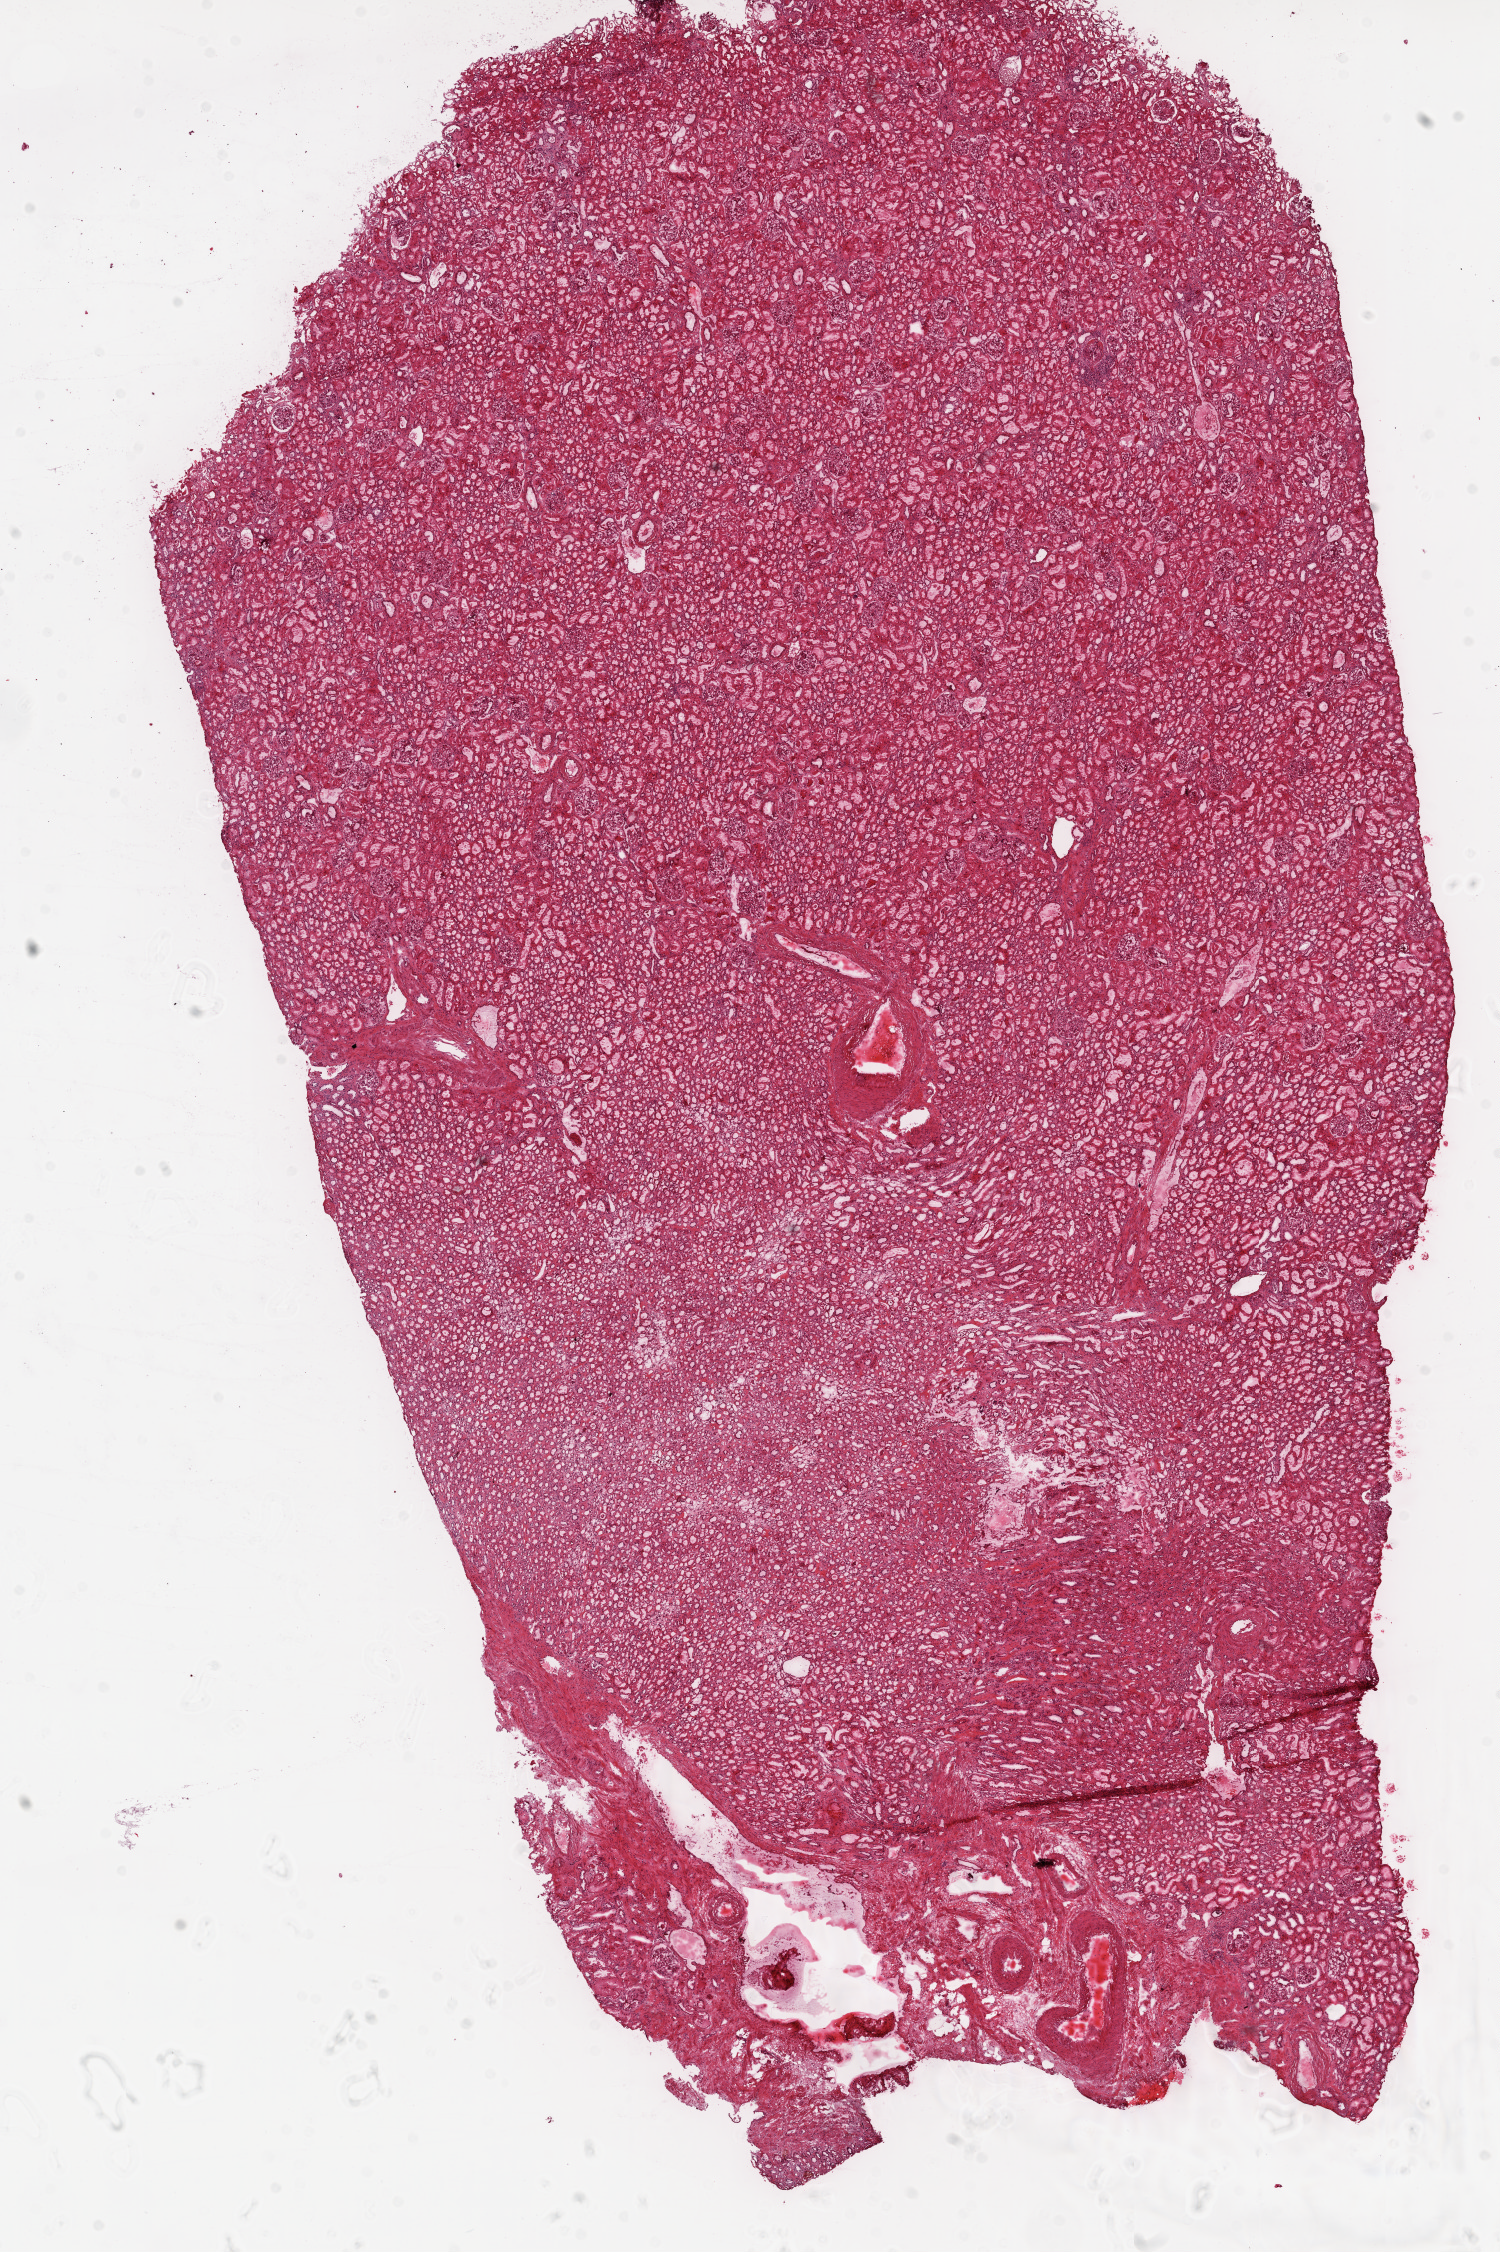
Digitized H&E-stained tissue section (whole slide) — low-resolution overview of the scanned area, about 12.0 x 18.1 mm, frozen section from the top of the tissue portion, solid tissue normal (non-tumour tissue) sample from the kidney. Male, age 72 years at initial diagnosis.
This section: solid tissue normal sample (biorepository sample class). Patient diagnosis: Clear cell adenocarcinoma, NOS.